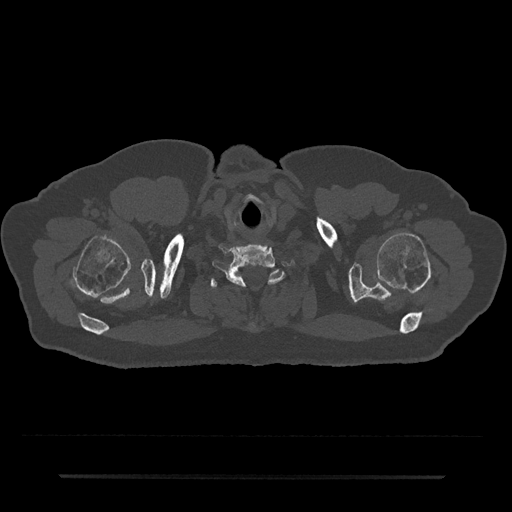
CT including the spine, one axial slice; bone window (W 1800 / L 400 HU); 0.5 mm slice thickness; 512 × 512 image matrix, field of view 437 × 437 mm. Patient: male, 69 years. From the clinical record (not read from this slice): primary cancer: prostate.
Annotated regions visible in this slice (semi-automatic segmentation, software-assisted and operator-edited):
- T1 vertebra: bounding box <211,269,281,328> (left, top, right, bottom; pixels)